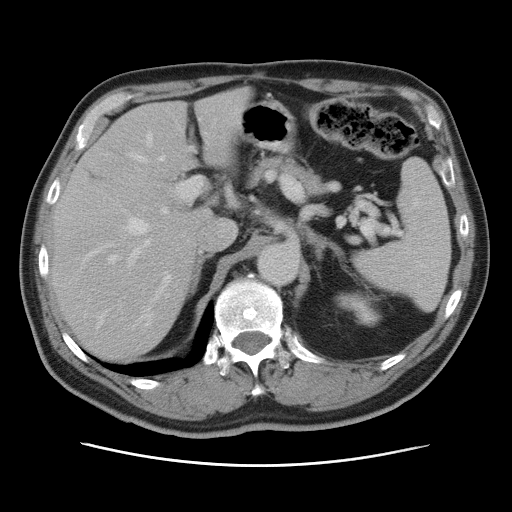
Contrast-enhanced abdominal CT, one axial slice. Position 52 of 80 along the scan axis. 120 kVp. Intravenous contrast given. Soft-tissue window (W 400 / L 40 HU). 5 mm slice thickness. 512 × 512 image matrix, field of view 370 × 370 mm. Male patient, age 69 years. Case-level facts recorded for this patient, not image findings: diagnosis: colorectal cancer liver metastases, imaged before liver resection; multiple liver metastases: no; largest metastasis: 5 cm; disease in both lobes: yes.
Annotated regions visible in this slice (outlined manually by an expert reader):
- hepatic veins: bounding box <88,134,166,325> (left, top, right, bottom; pixels)
- liver: <52,92,248,361>
- planned liver remnant (the part of the liver to remain after resection): <51,92,248,360>
- portal vein (with intrahepatic branches): <108,119,218,312>